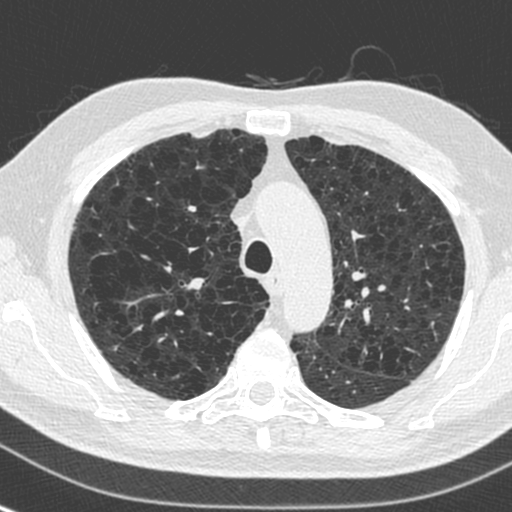
Chest CT (low-dose screening protocol), one axial image, first (baseline) screen, lung window (W 1500 / L -600 HU), standard (soft-tissue) reconstruction kernel (C). Male, age 73 years at enrolment. Current smoker at enrolment.
Expert-annotated lung lesion, bounding box (x1, y1, x2, y2) in pixels: (148, 248, 195, 286). Screening reader's record for this exam: no non-calcified nodule ≥4 mm recorded. Participant outcome: lung cancer diagnosed 446 days after this screen — squamous cell carcinoma, NOS, right upper lobe, stage IA (AJCC 6th edition), 10 mm at pathology.